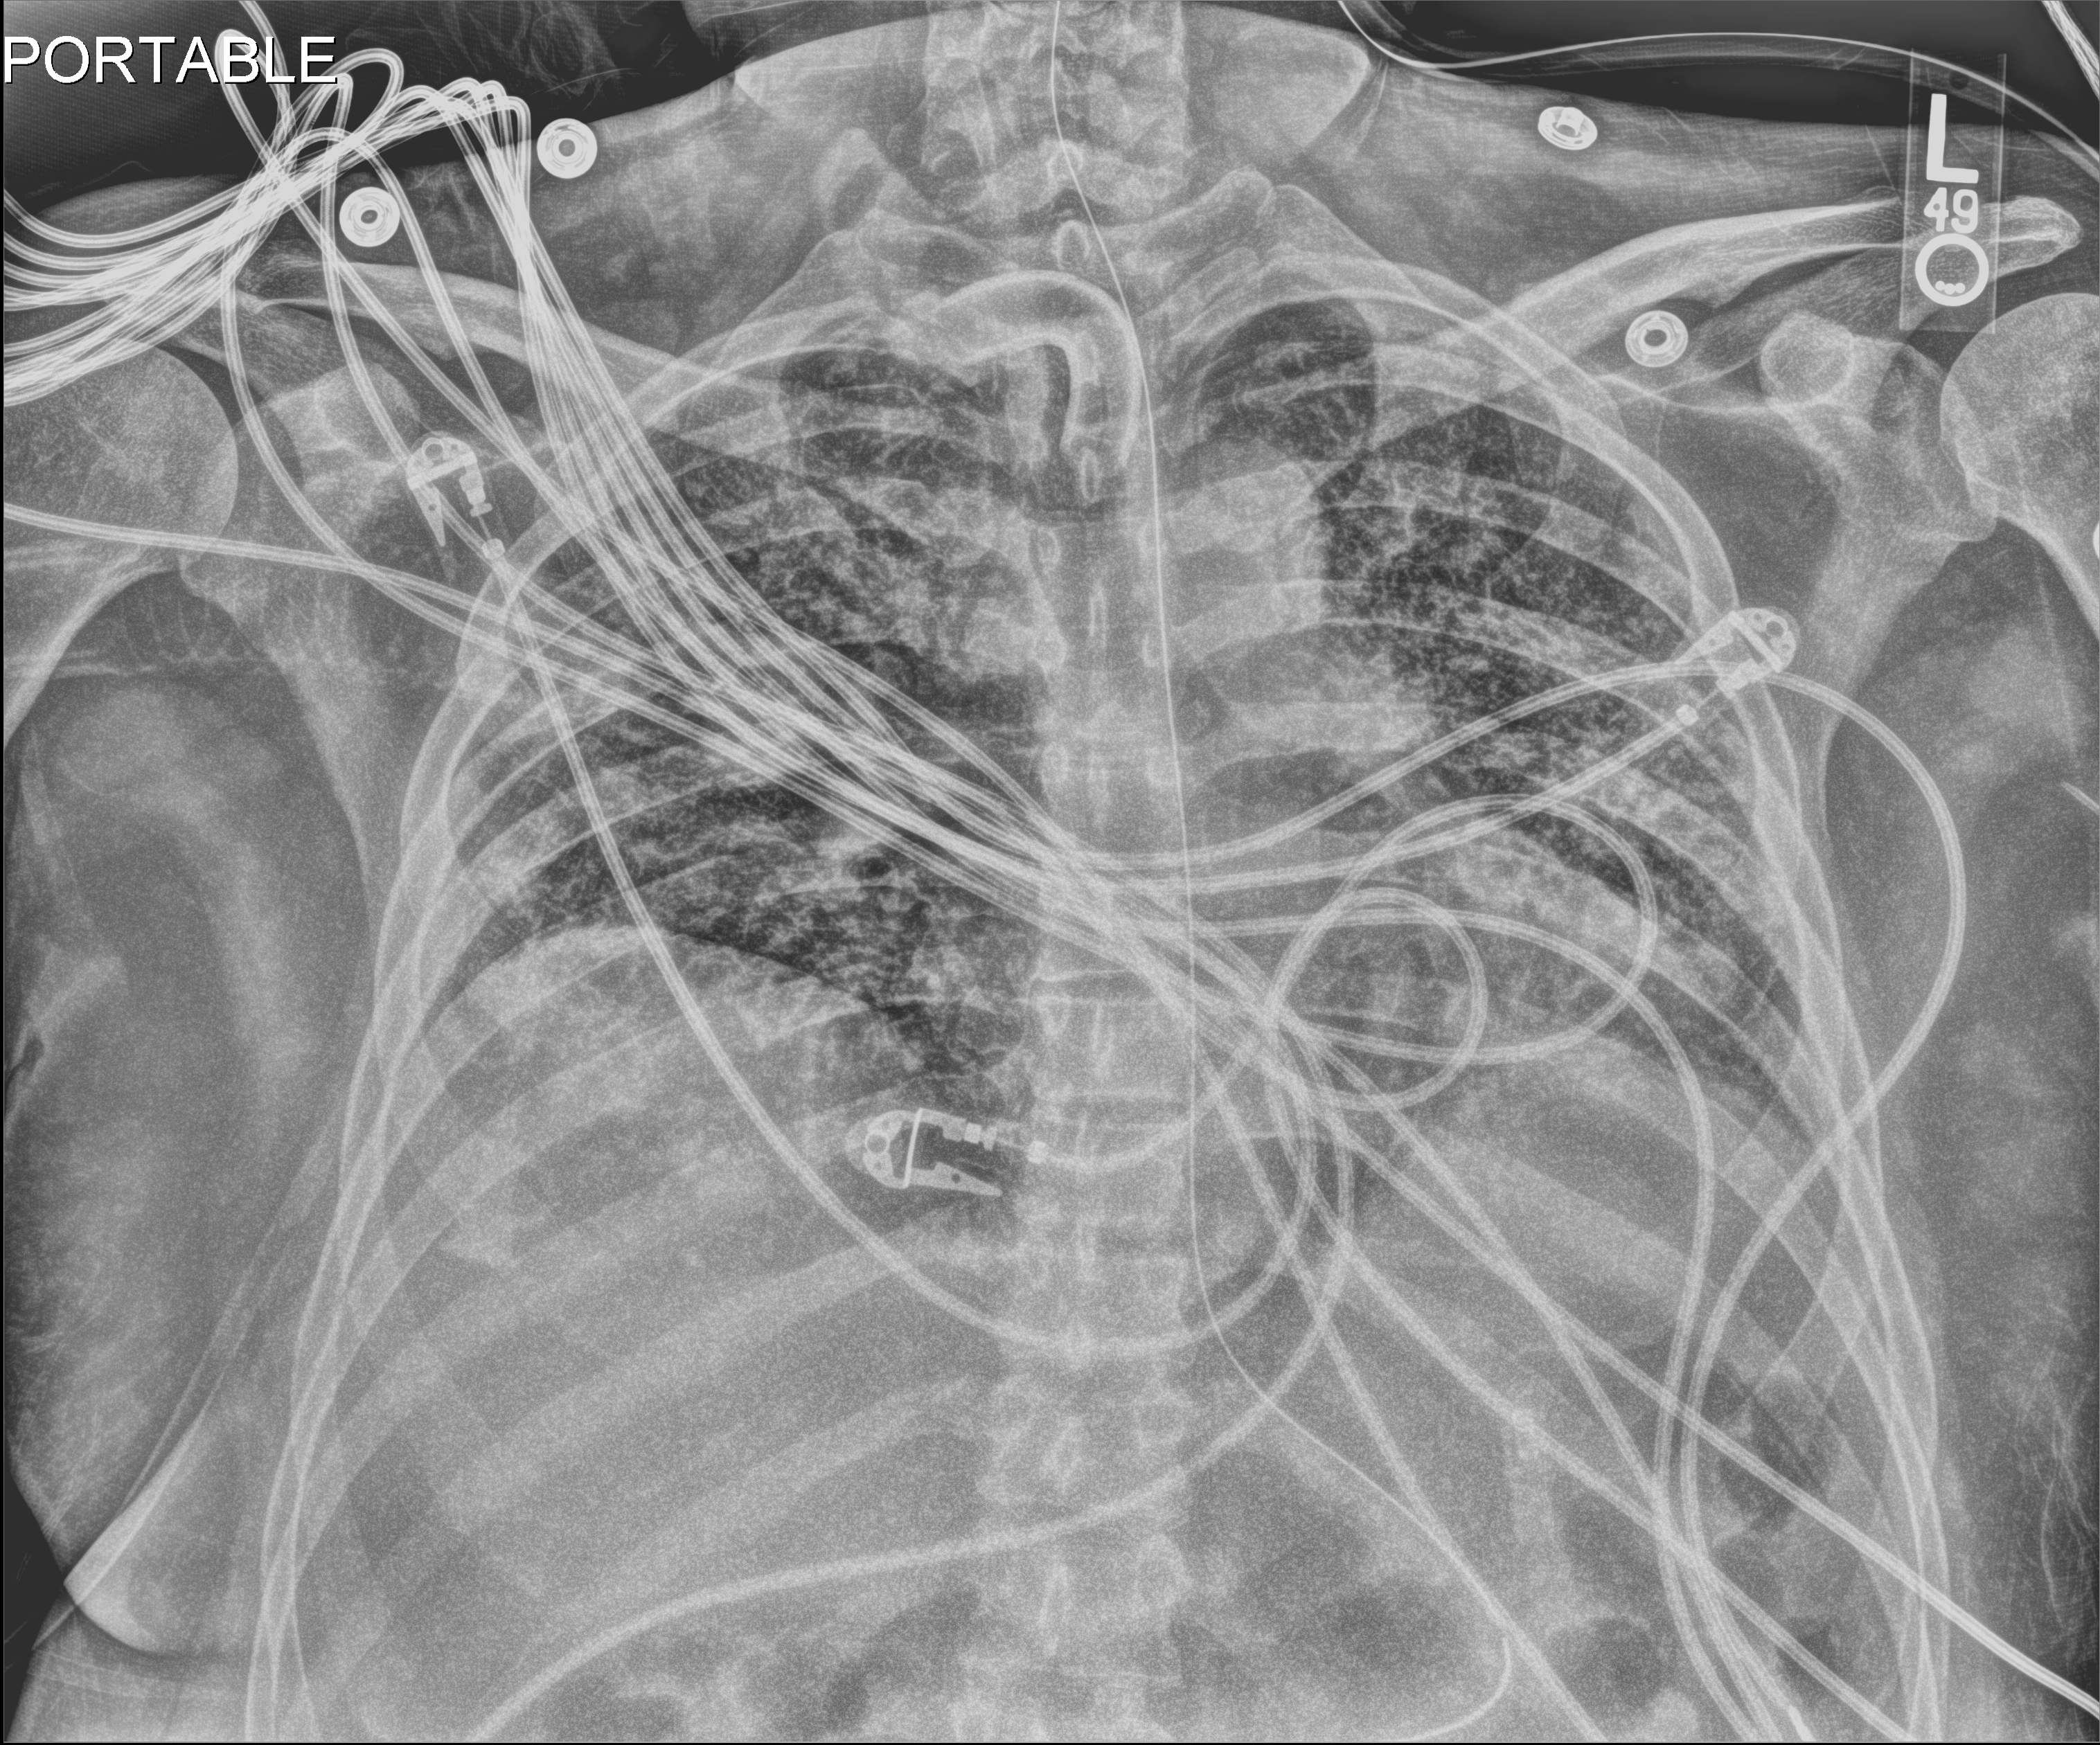
Portable chest radiograph; anteroposterior (AP) projection. Male patient hospitalised with COVID-19, age 18–59 years.
Hospital-stay facts (about this admission, not read from this image; timing relative to this image not recorded): mechanically ventilated during this hospital stay: yes; admitted to intensive care during this hospital stay: yes; length of hospital stay: 96 days.